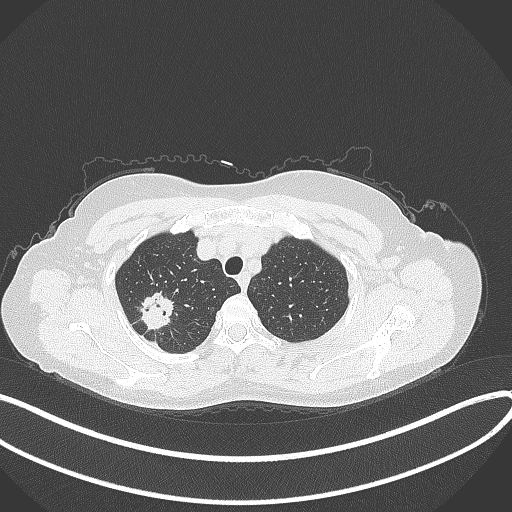
Chest CT, one axial slice. 120 kVp. Lung window (W 1500 / L -600 HU). 1 mm slice thickness. 512 × 512 image matrix, field of view 400 × 400 mm. Female patient, age 50 years. From the clinical record (not read from this slice): clinical TNM (as recorded): T1c N0 M0; histopathological grade: G2-3.
Annotated regions visible in this slice (rectangle marked by the reading radiologist):
- lung tumour (recorded histology: adenocarcinoma): bounding box [x1, y1, x2, y2] px = [135, 292, 180, 333]